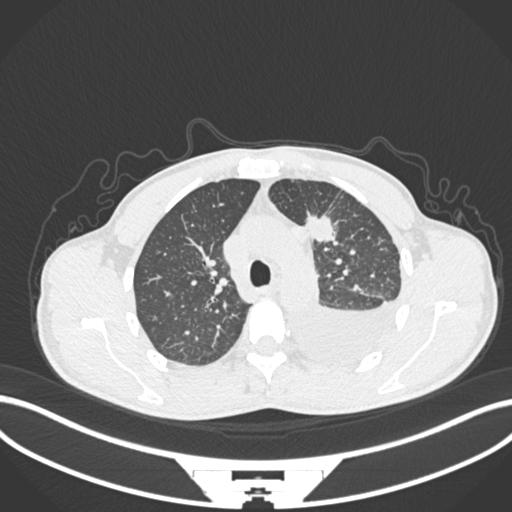
Chest CT, one axial slice; slice 157 of 244 in the series (ordered by position); reconstruction kernel B30f; 120 kVp; lung window (W 1500 / L -600 HU); 1 mm slice thickness; 512 × 512 image matrix. Male patient, age 49 years. From the clinical record (not read from this slice): clinical TNM (as recorded): T1c N1 M1.
Annotated regions visible in this slice (bounding box drawn by a radiologist):
- lung tumour (recorded histology: adenocarcinoma): bounding box (x1, y1, x2, y2) in pixels: (305, 211, 340, 246)